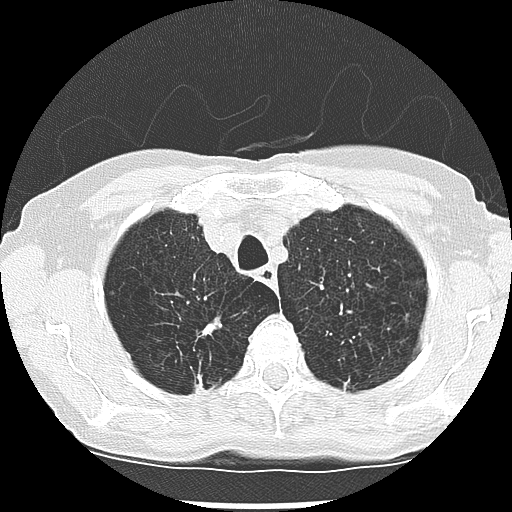
Low-dose screening chest CT, one axial slice. Slice 226 of 265 in the series (ordered by position). Reconstruction kernel LUNG. Lung window (W 1500 / L -600 HU). 2.5 mm slice thickness. 512 × 512 image matrix.
Outlined on this slice (manually delineated by an expert):
- lesion 1 (nodule, upper lobe of right lung): bounding box [x1, y1, x2, y2] px = [195, 376, 203, 391]
- lesion 2 (tumor, upper lobe of right lung): [204, 324, 215, 333]